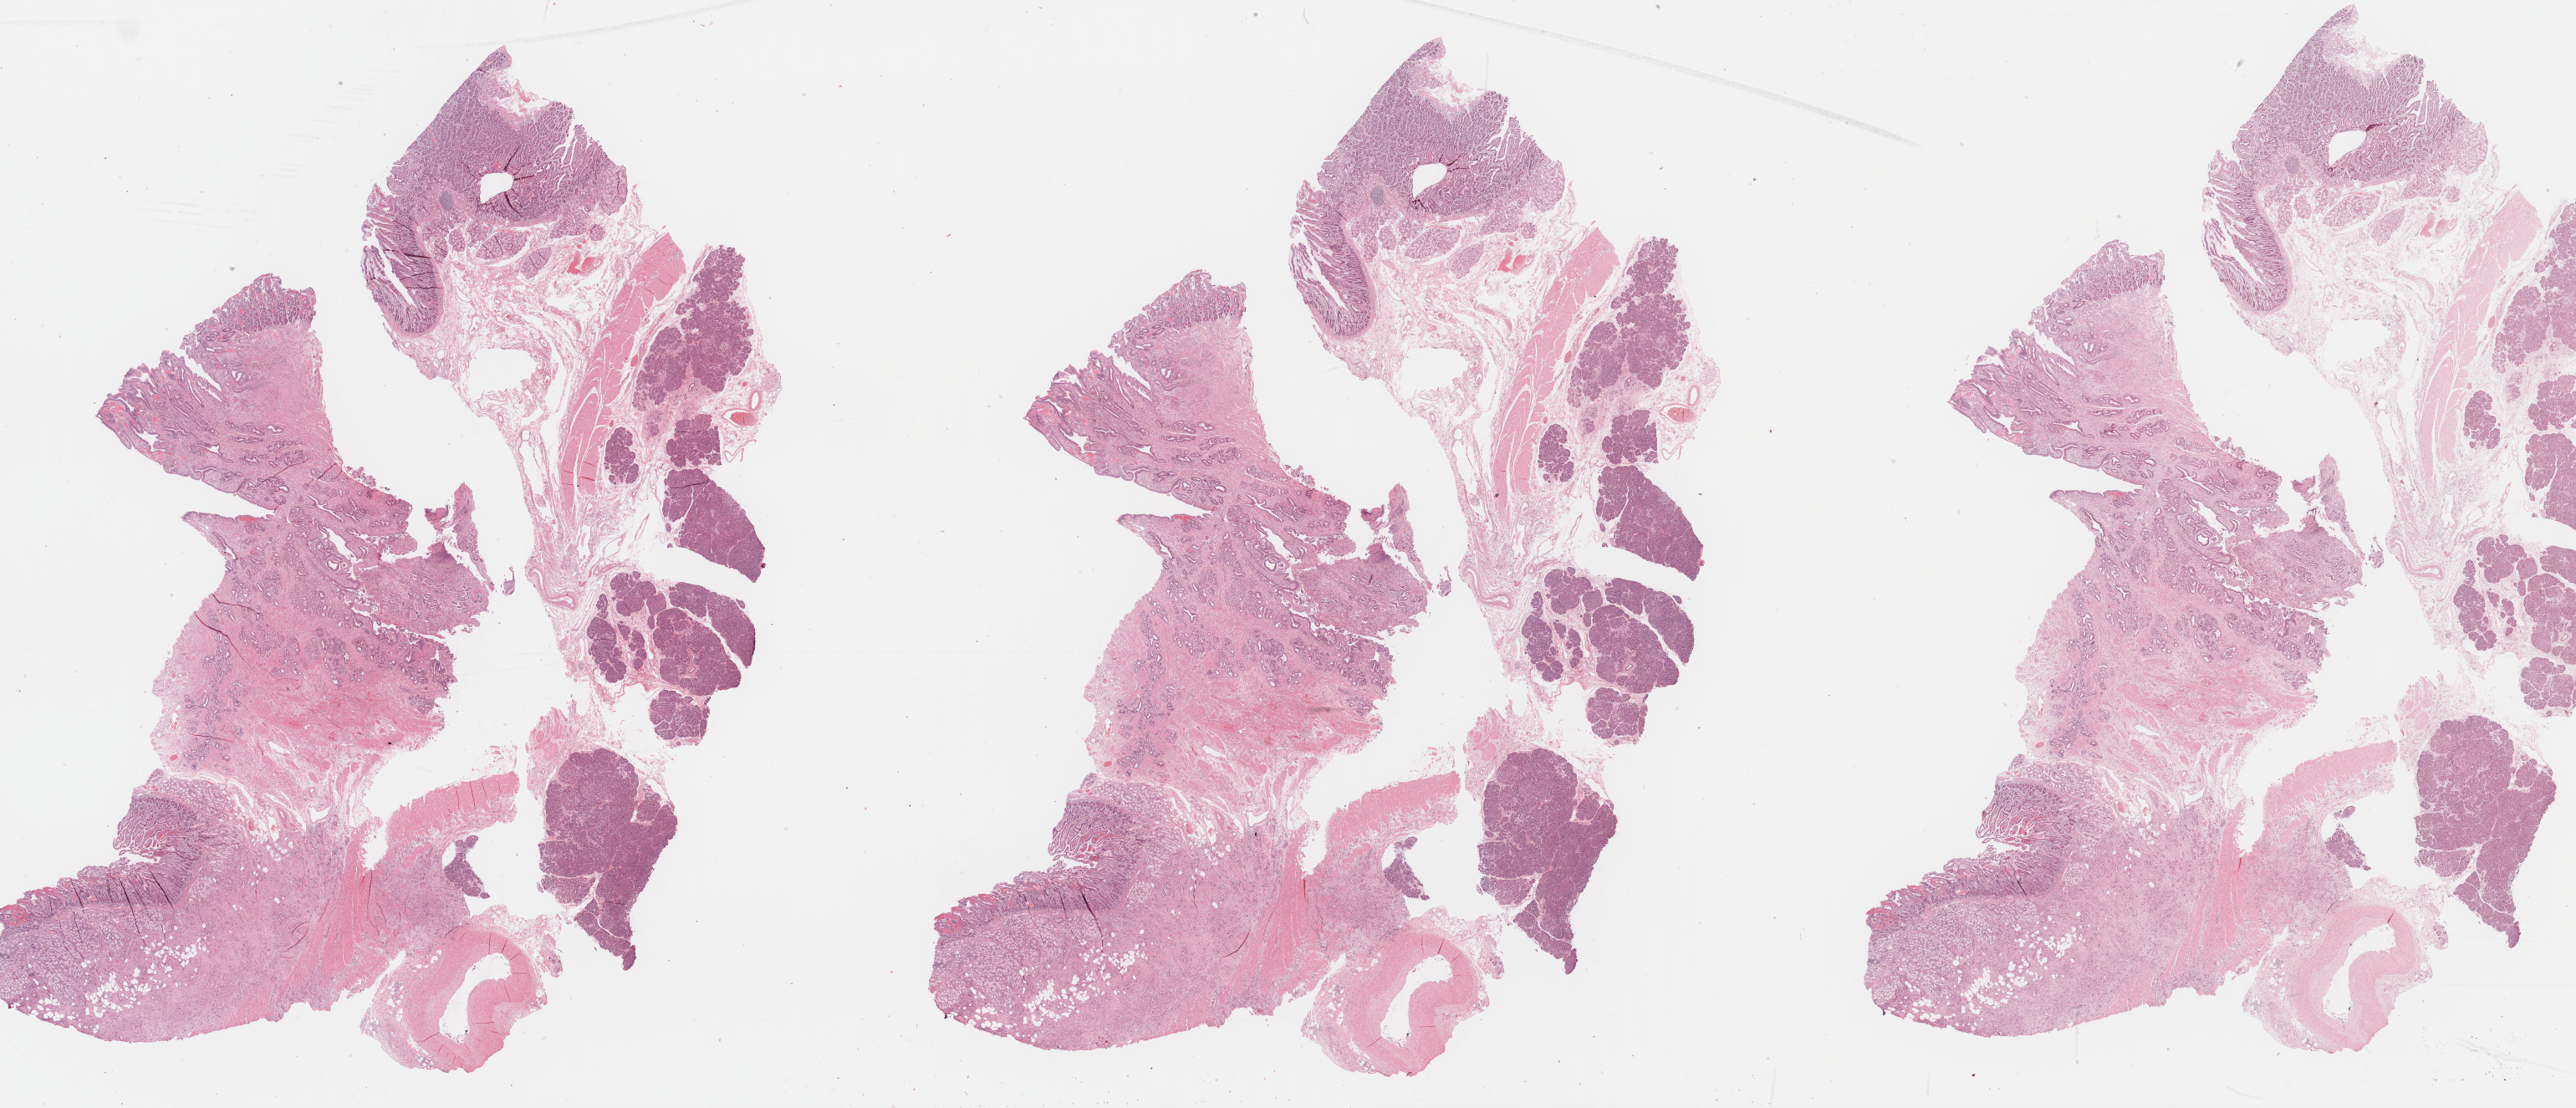
Hematoxylin and eosin (H&E) stained whole-slide image — shown as a low-resolution overview of the whole scanned area (about 49.8 x 21.4 mm, slide scanned at 40x). FFPE section. Pancreas, primary tumour sample. Male patient; age at initial diagnosis 60 years. Histologic grade: G2 (moderately differentiated).
- lymph nodes positive (case pathology): 6 of 6 examined
- AJCC pathologic stage: IIB (6th edition)
- histologic diagnosis: Infiltrating duct carcinoma, NOS (head of pancreas)